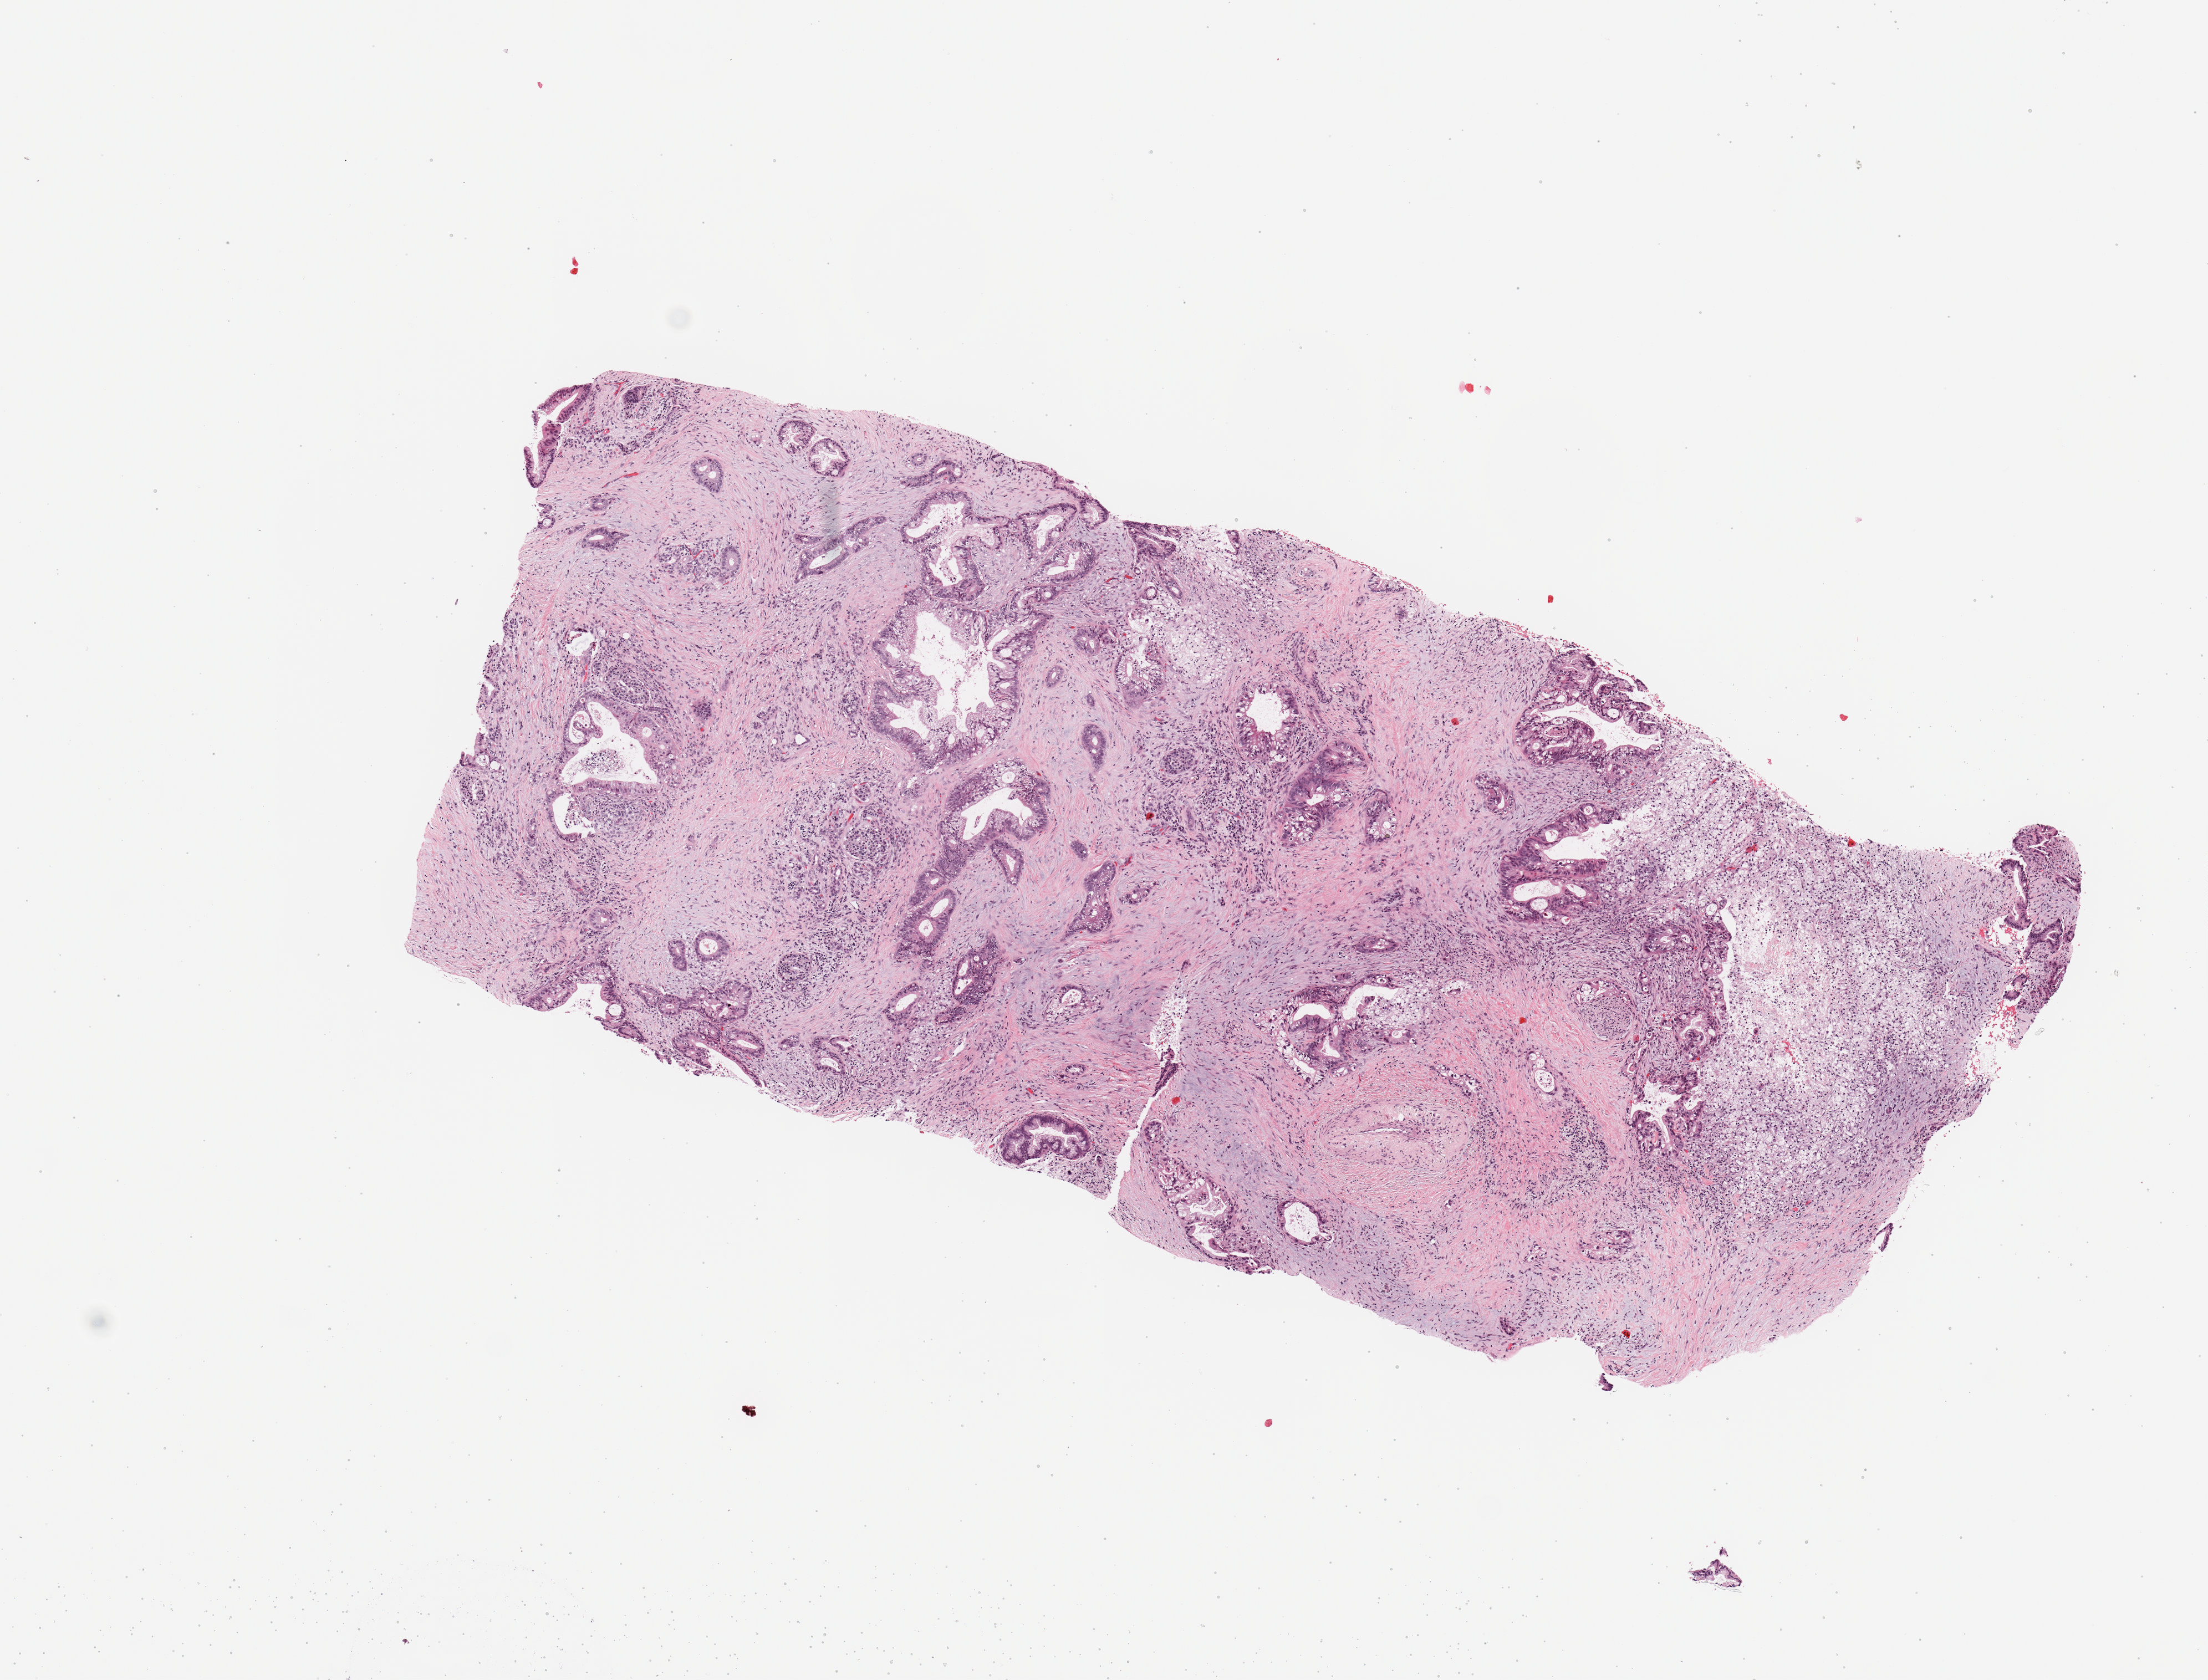
Whole-slide histology image, Hematoxylin and eosin (H&E) stained — a low-resolution overview of the entire scanned area, about 7.9 x 6.0 mm. Tumour tissue sample, sampled site: pancreas. Female, 78 y/o. Histologic grade: G2 (moderately differentiated). Slide review estimates, as recorded: tumour nuclei 50%, necrosis 10%.
AJCC pathologic stage: IIB. Diagnosis: Infiltrating duct carcinoma, NOS. Primary tumour site (as recorded): body.